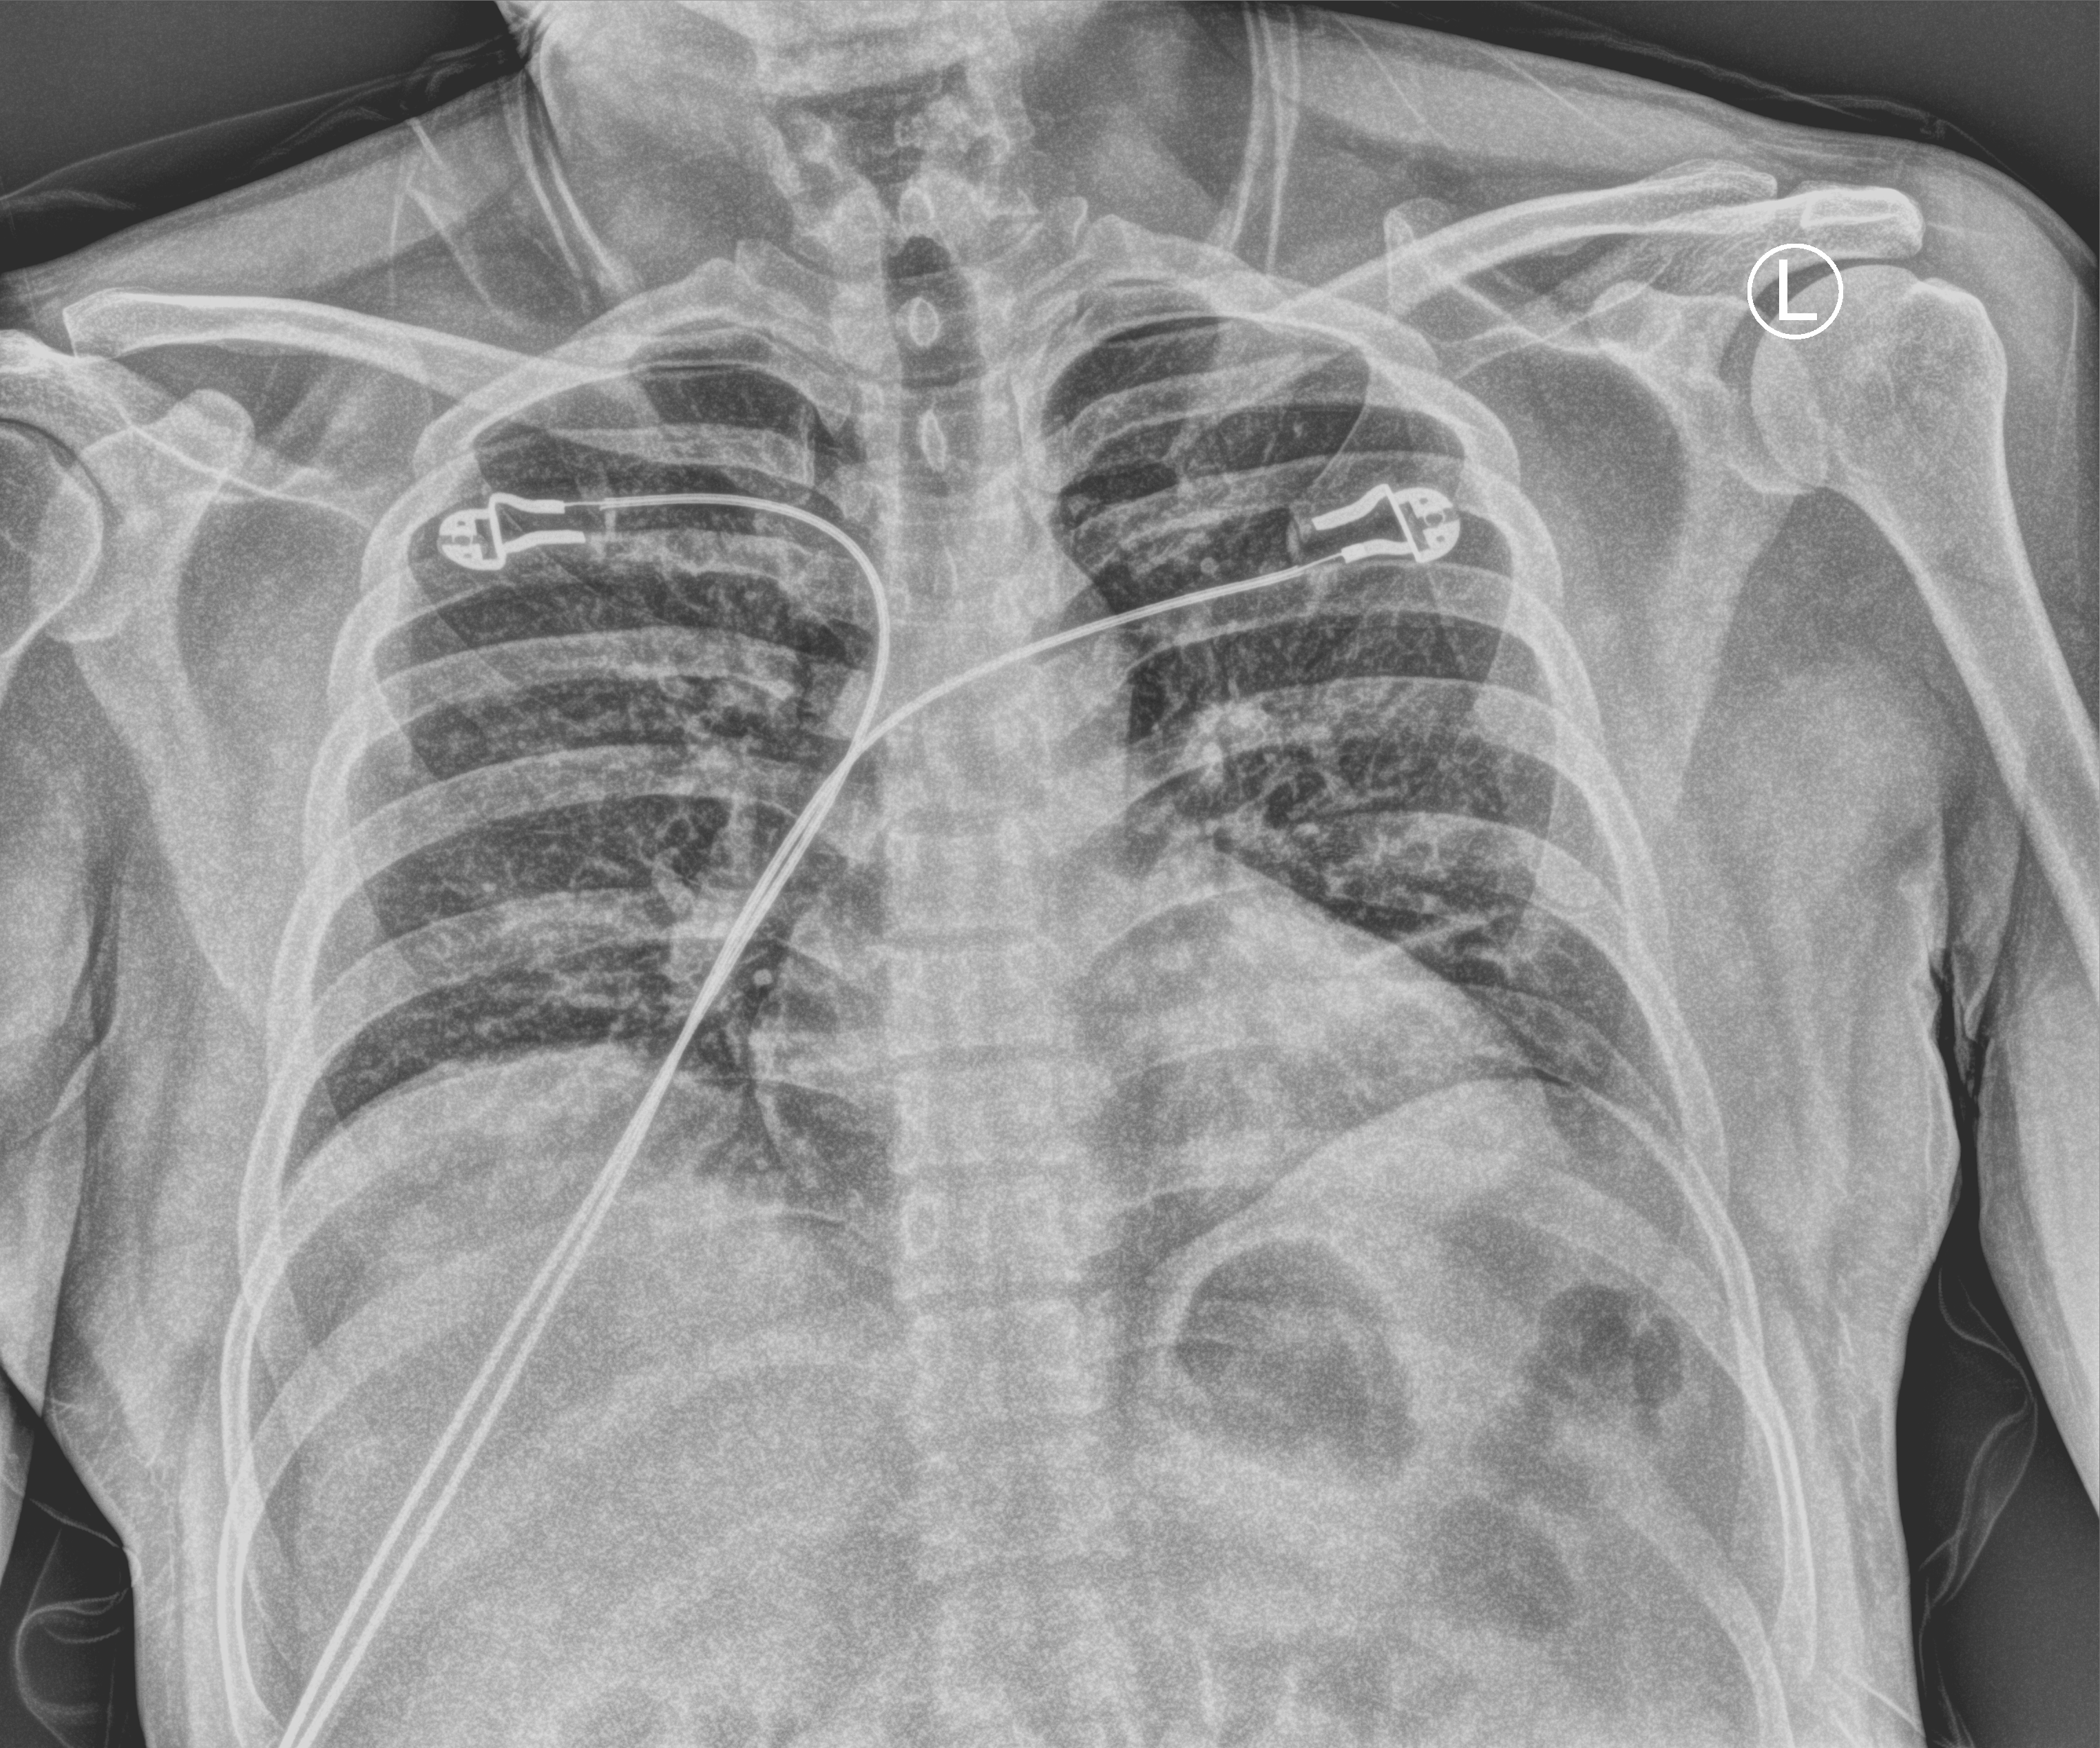
Chest X-ray (portable); anteroposterior (AP) projection. Patient hospitalised with COVID-19; male, aged 18–59 years.
From the hospital-stay record, not from the radiograph (when in the stay this image was taken is not recorded): length of hospital stay: 7 days; admitted to intensive care during this hospital stay: no; mechanically ventilated during this hospital stay: no.